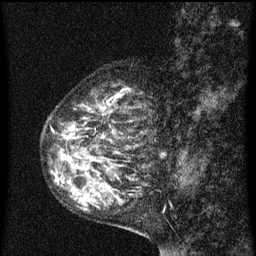
Breast MRI (dynamic contrast-enhanced), one sagittal slice; slice 25 of 60 in the series (ordered by position); dynamic contrast-enhanced series, image 2 of 3 at this slice position (ordered by acquisition); 1.5 T; TE 4.2 ms, TR 8 ms; 256 × 256 image matrix, field of view 180 × 180 mm. Patient: female, 55 years.
Annotated regions visible in this slice (semi-automatic segmentation, software-assisted and operator-edited):
- analysis volume of interest (the breast-tissue region the enhancement analysis was run in; not a lesion): bounding box [x1, y1, x2, y2] px = [42, 84, 157, 151]
- tumour enhancement mask (voxels above the 70 % enhancement threshold inside the analysis volume of interest): [62, 94, 125, 151]